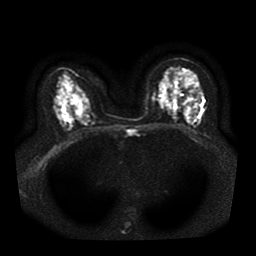
Breast MRI, one axial slice. Slice 20 of 41 in the series (ordered by position). Diffusion-weighted series; image 2 of 4 stored at this slice position (different b-values; order by instance number). 1.5 T. 256 × 256 image matrix. Female patient.
Annotated regions visible in this slice (manually delineated by an expert):
- tumour on diffusion-weighted imaging: box from (x=188, y=90) to (x=193, y=93) px